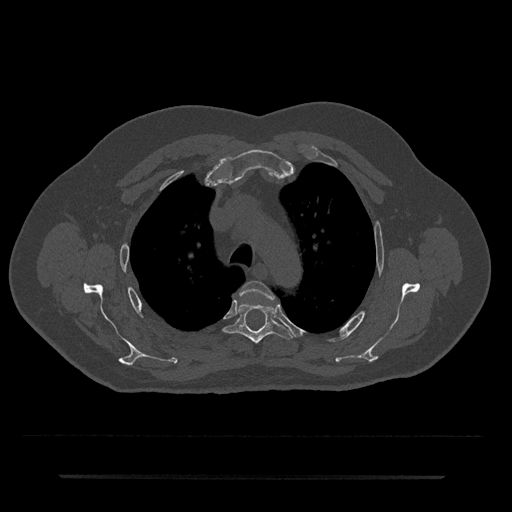
CT including the spine, one axial slice; slice 536 of 797 in the series (ordered by position); reconstruction kernel Br40s/3; bone window (W 1800 / L 400 HU); 0.5 mm slice thickness; 512 × 512 image matrix. Patient: male, 69 years. From the clinical record (not read from this slice): primary cancer: prostate.
Outlined on this slice (semi-automatic segmentation, software-assisted and operator-edited):
- T3 vertebra: bounding box <240,280,274,300> (left, top, right, bottom; pixels)
- T4 vertebra: <222,303,293,344>